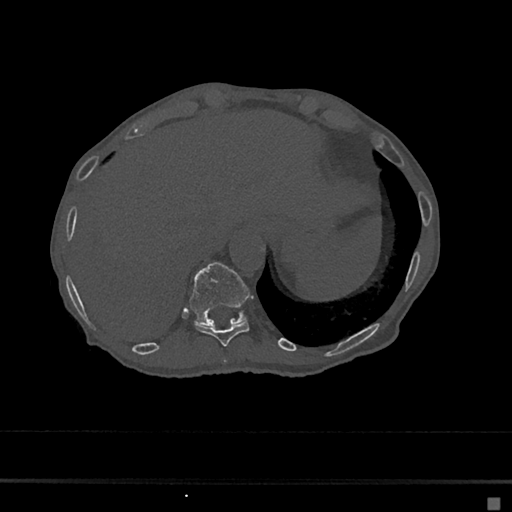
CT including the spine, one axial slice. Position 205 of 797 along the scan axis. Bone window (W 1800 / L 400 HU). 0.5 mm slice thickness. 512 × 512 image matrix. Female patient, age 68 years. From the clinical record (not read from this slice): primary cancer: renal.
Outlined on this slice (semi-automatically segmented with operator editing):
- T10 vertebra: bounding box <194,320,249,347> (left, top, right, bottom; pixels)
- T11 vertebra: <190,262,252,326>
- T9 vertebra: <222,359,227,364>